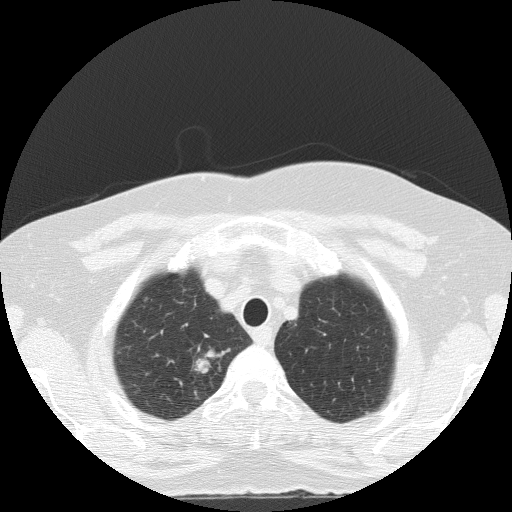
Low-dose screening chest CT, one axial slice; slice 116 of 133 in the series (ordered by position); reconstruction kernel FC51; 120 kVp; lung window (W 1500 / L -600 HU); 2 mm slice thickness; 512 × 512 image matrix, field of view 320 × 320 mm.
Annotated regions visible in this slice (expert manual segmentation):
- lesion 1 (tumor, upper lobe of right lung): bounding box (x1, y1, x2, y2) in pixels: (195, 349, 223, 374)